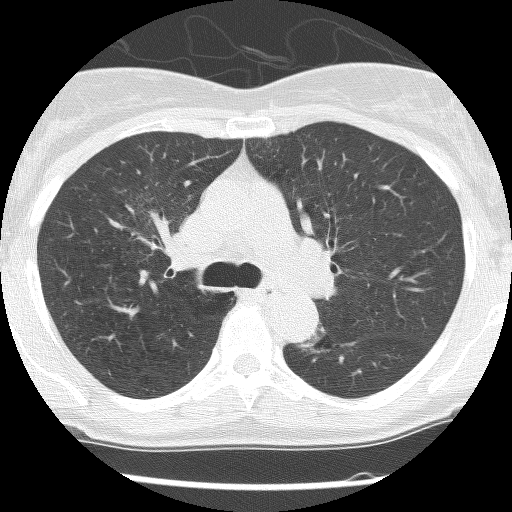
Chest CT (low-dose screening protocol), one axial image. Second screening round (one year after baseline). Lung window (W 1500 / L -600 HU). 2.5 mm slice thickness. Slice 44 of 120 in the series. 512 × 512 image matrix. Female participant, aged 62 years at enrolment.
Expert reader's lesion annotation, bounding box [x1, y1, x2, y2] px = [294, 320, 351, 363]. Reader record for this screening exam (exam-level; its link to the box is not recorded): non-calcified nodule or mass ≥4 mm, right upper lobe, 30 × 30 mm, poorly defined margins, ground glass attenuation, pre-existing on the prior screen: yes; interval growth: no. Note: the box lies in the patient's left hemithorax on this image, whereas the reader's record names the right lung; they may be different findings. Official screen result: positive, no significant change: stable abnormalities potentially related to lung cancer, unchanged since the prior screening exam.